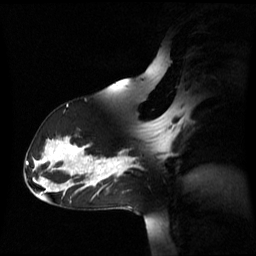
Breast MRI (dynamic contrast-enhanced), one sagittal slice. Slice 38 of 60 in the series (ordered by position). Dynamic contrast-enhanced series, image 2 of 3 at this slice position (ordered by acquisition). 1.5 T. TE 4.2 ms, TR 8.4 ms. 2.6 mm slice thickness. 256 × 256 image matrix. Patient: female, 39 years. Case-level facts recorded for this patient, not image findings: setting: breast cancer imaged before/during neoadjuvant chemotherapy; receptor status: triple-negative.
Structures marked on this image (semi-automatically segmented with operator editing):
- analysis volume of interest (the breast-tissue region the enhancement analysis was run in; not a lesion): box from (x=105, y=157) to (x=131, y=179) px
- tumour enhancement mask (voxels above the 70 % enhancement threshold inside the analysis volume of interest): (x=105, y=157)–(x=128, y=176)